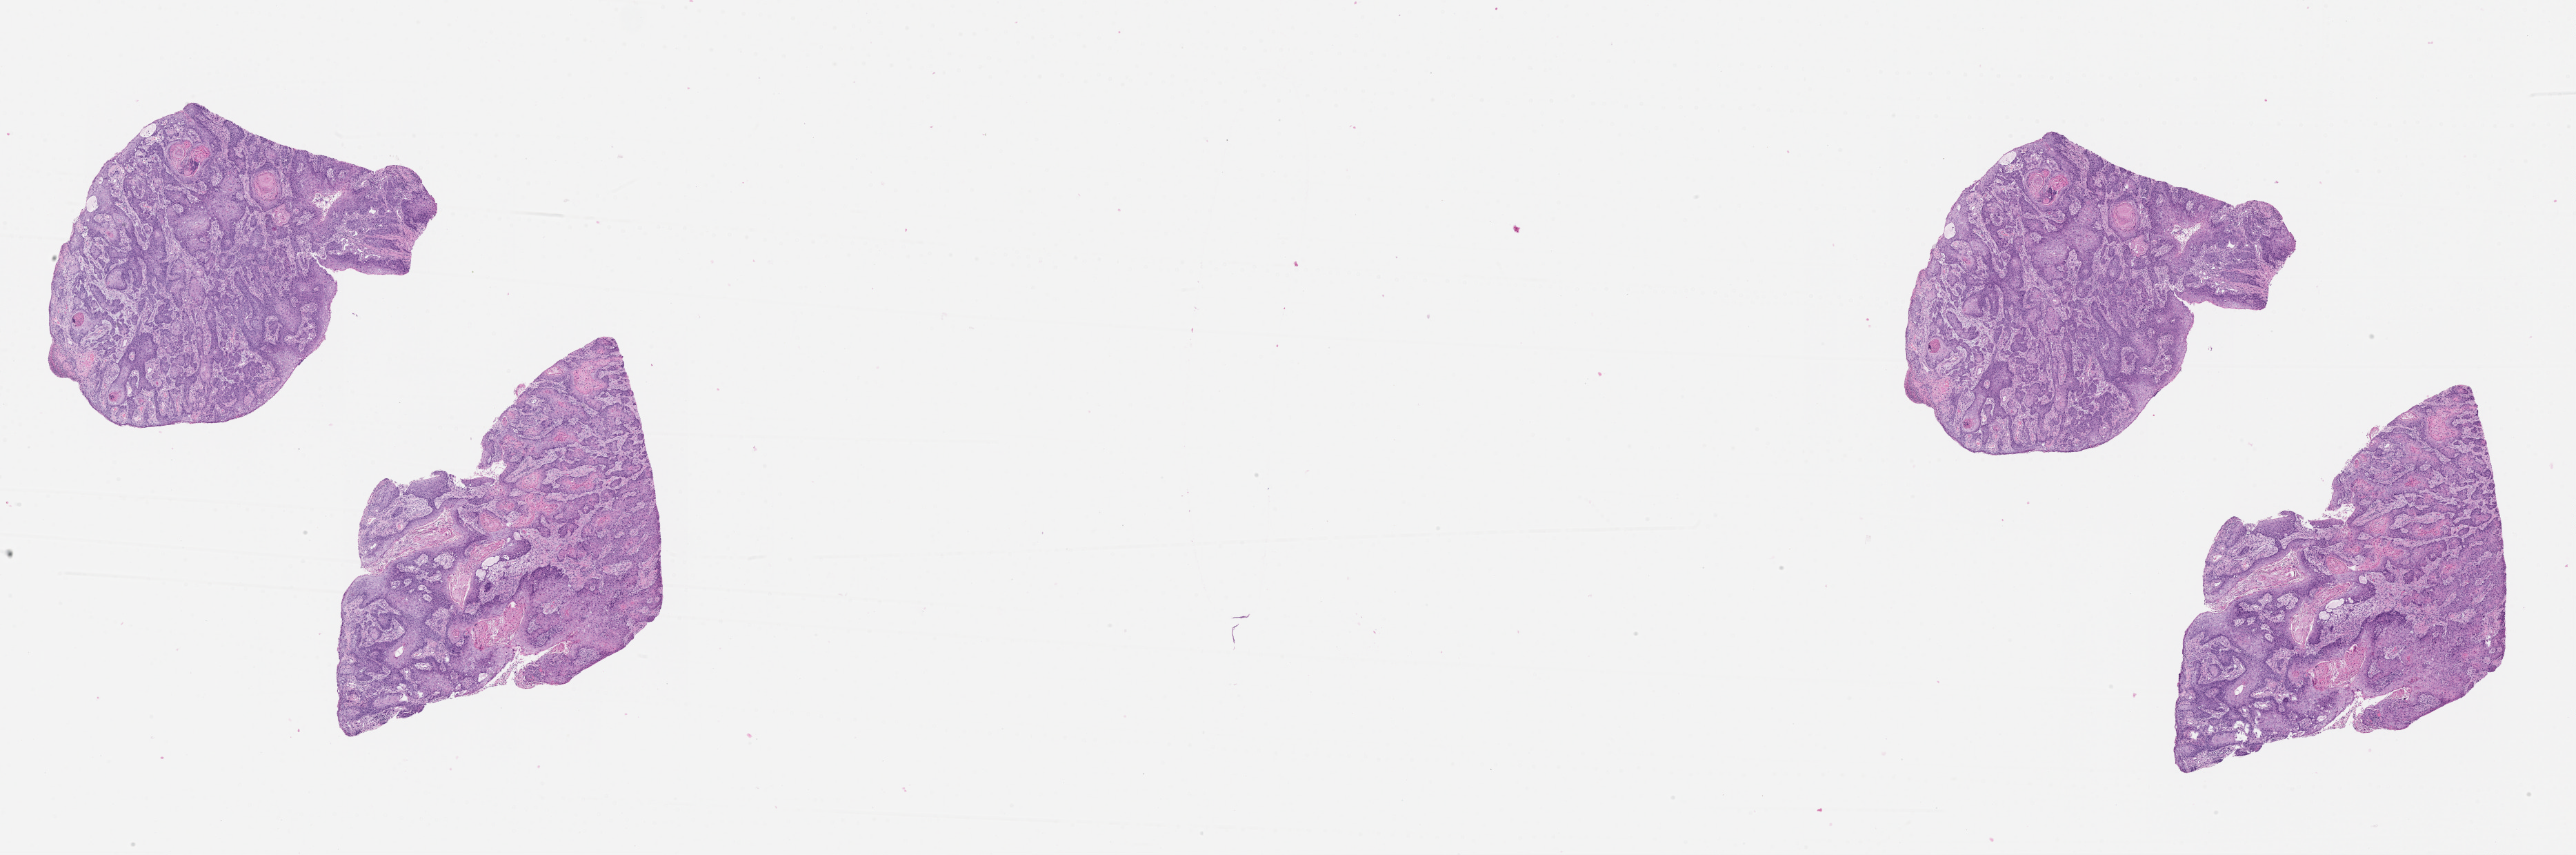
H&E-stained whole-slide image — whole scanned area (about 30.1 x 10.0 mm, from a 20x scan) shown as a low-resolution overview, tumour tissue sample, sampled site: tonsil. Female, 61 y/o. Histologic grade: G2 (moderately differentiated). Composition of this section per pathologist review: tumour nuclei 85%, necrosis 3%.
- AJCC pathologic stage: IVB
- primary tumour site (as recorded): oropharynx
- diagnosis: Squamous cell carcinoma, NOS (tonsil, NOS)